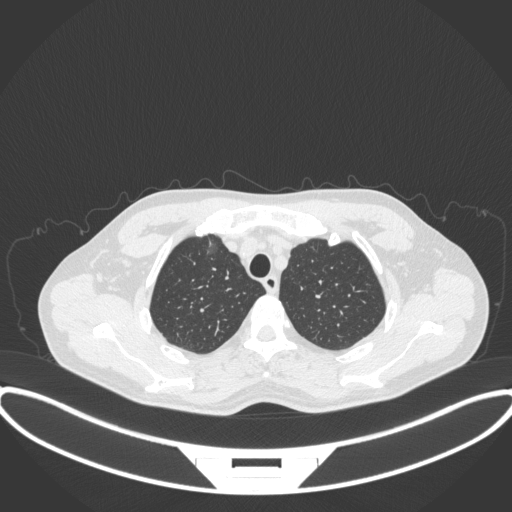
Chest CT, one axial slice; position 307 of 395 along the scan axis; reconstruction kernel B31f; 120 kVp; lung window (W 1500 / L -600 HU); 1 mm slice thickness; 512 × 512 image matrix, field of view 424 × 424 mm. Patient: male, 60 years. Case-level facts recorded for this patient, not image findings: clinical TNM (as recorded): T1c N0 M0.
Annotated regions visible in this slice (bounding box drawn by a radiologist):
- lung tumour (recorded histology: adenocarcinoma): bounding box <202,228,221,259> (left, top, right, bottom; pixels)